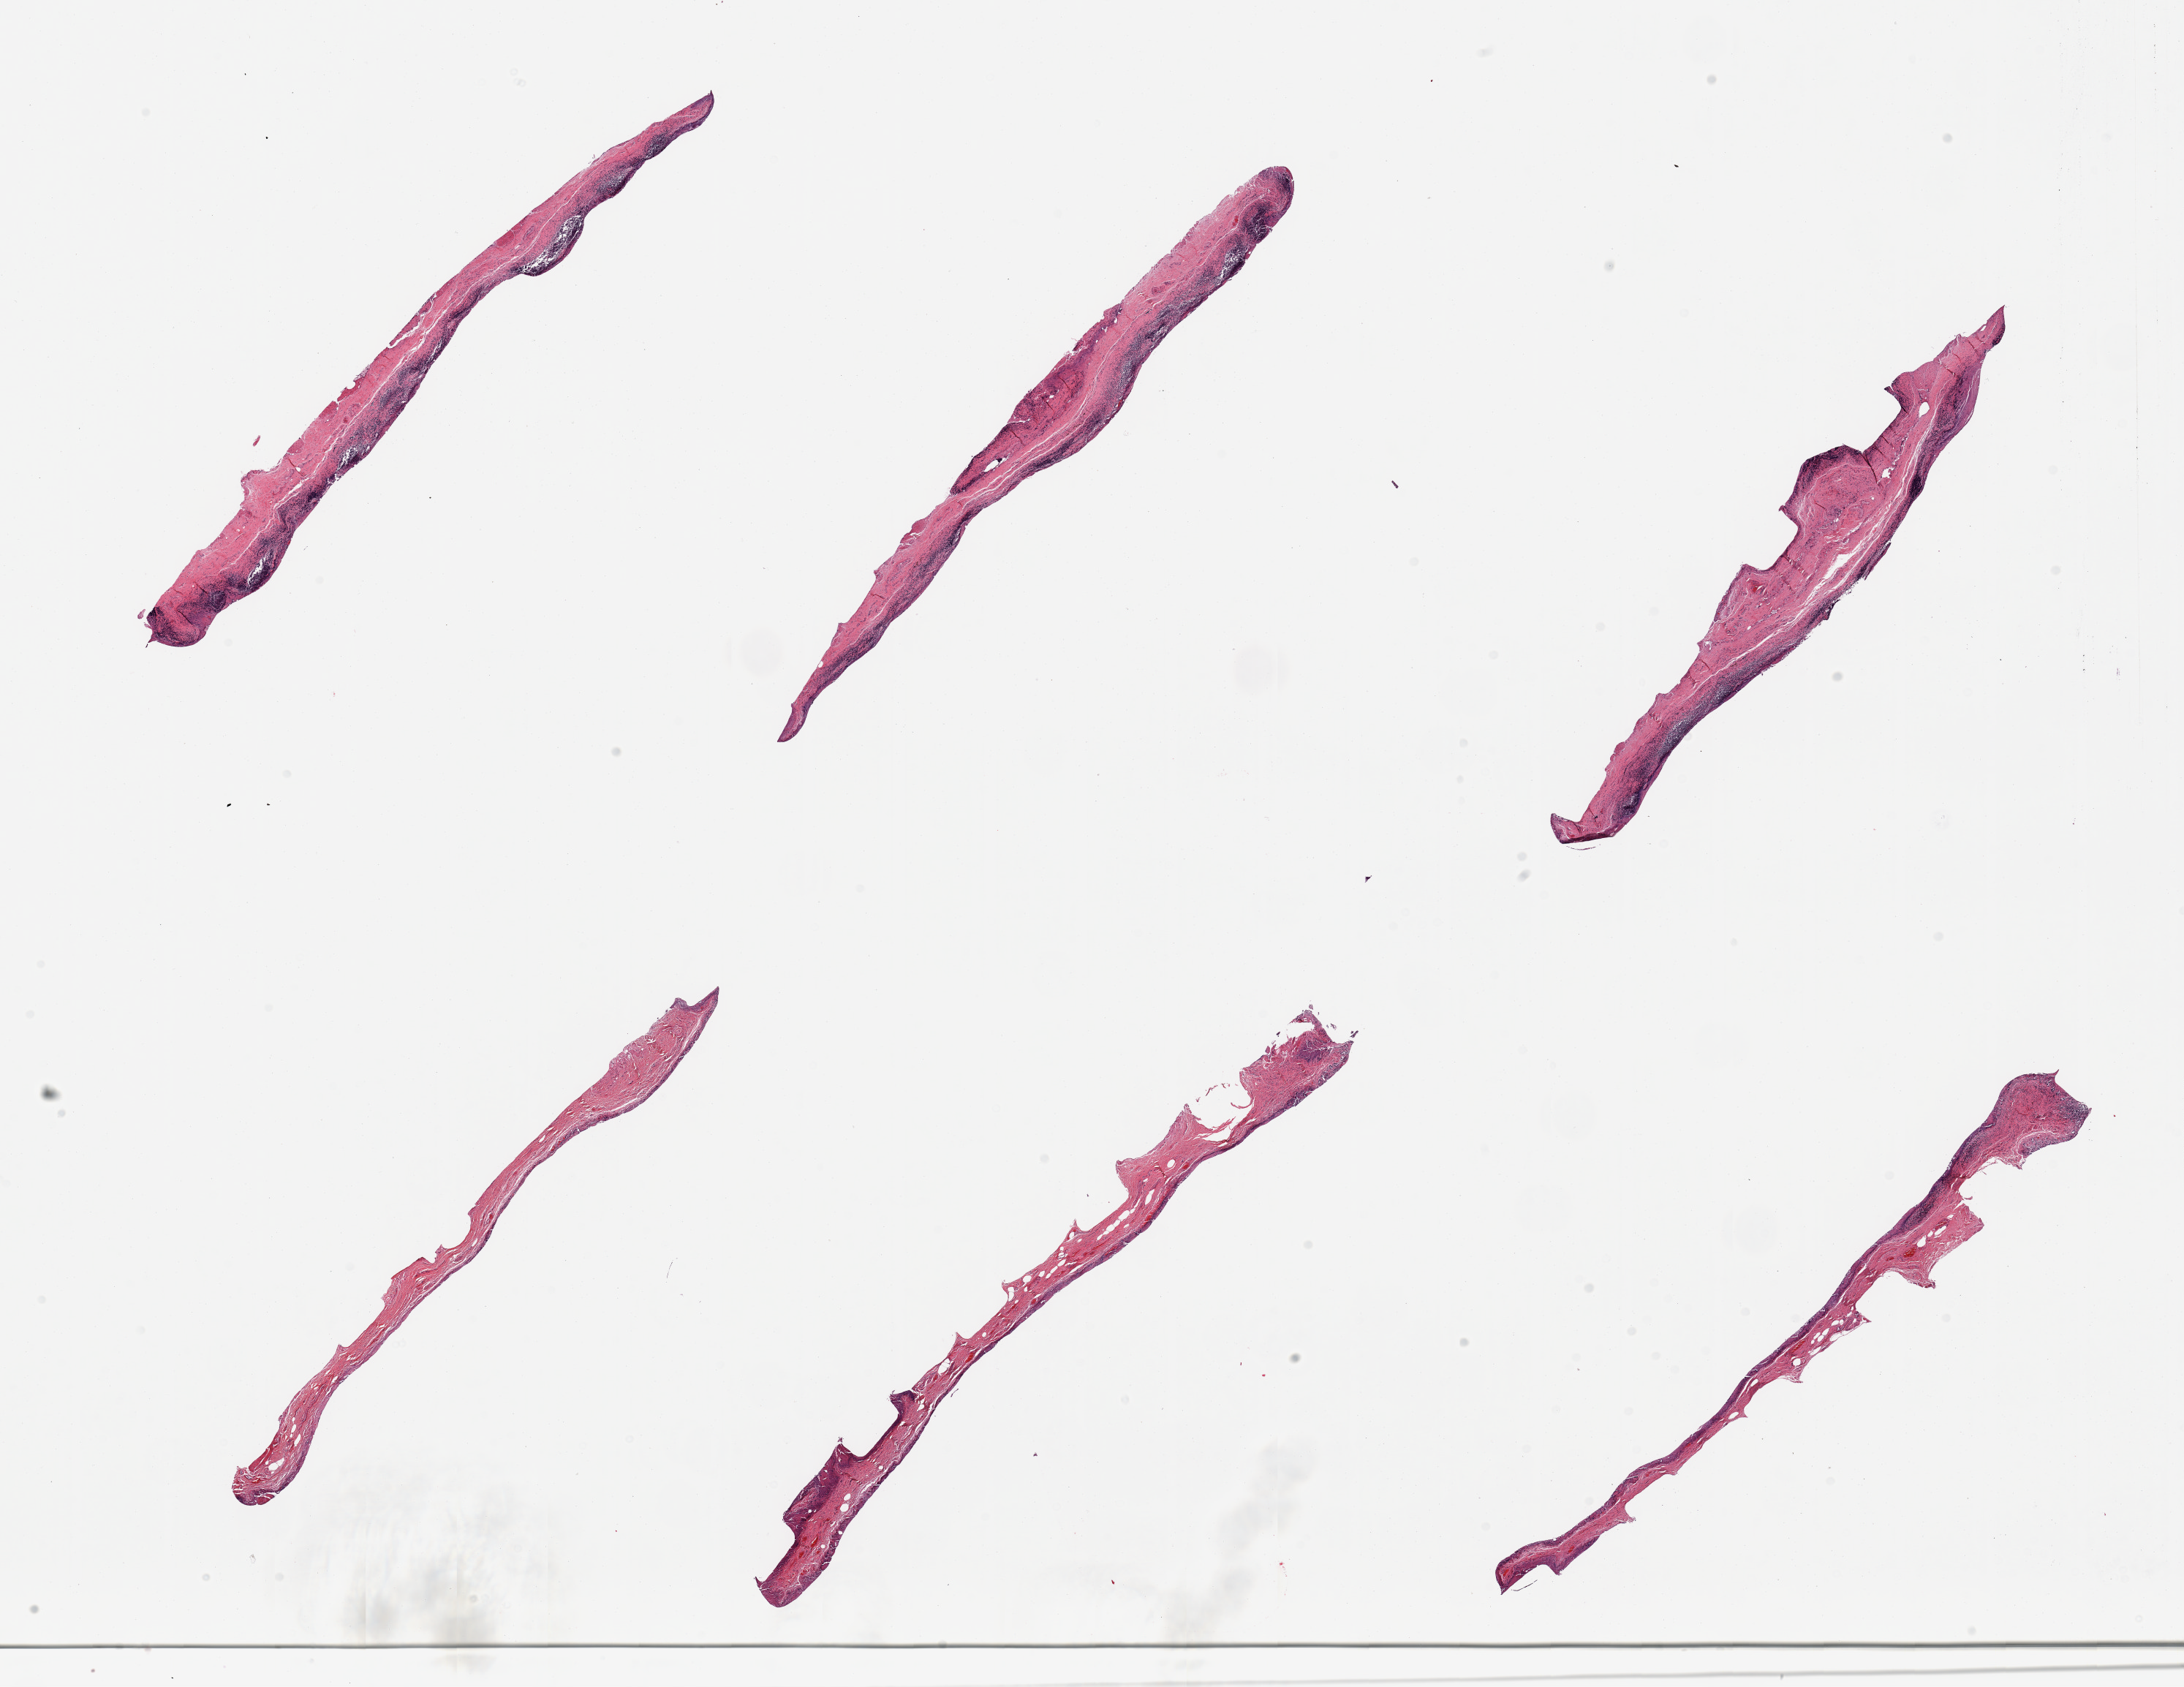
Whole-slide image, hematoxylin and eosin (H&E) stain — shown as a low-resolution overview of the whole scanned area (about 23.6 x 18.2 mm). PAXgene-fixed, paraffin-embedded tissue. Section of ileum (target tissue). Tissue donor sample. Donor: male.
Pathologist's review note for this sample: 6 pieces, glandular mucosal elements sloughed, resdiual lymphoid aggregates are ~20-30%.